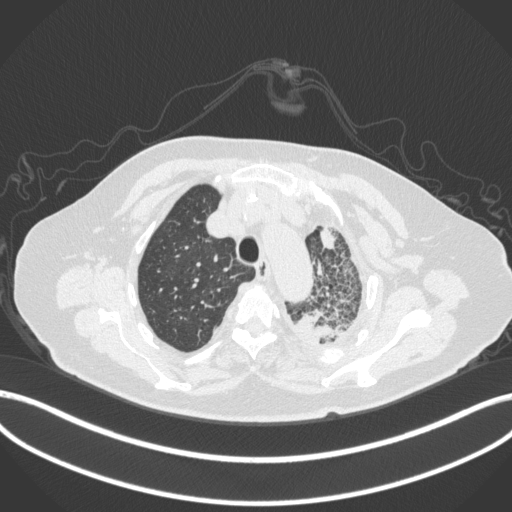
Chest CT, one axial slice. Position 315 of 399 along the scan axis. Reconstruction kernel B31f. 120 kVp. Lung window (W 1500 / L -600 HU). 512 × 512 image matrix, field of view 400 × 400 mm. Patient: female, 75 years. From the clinical record (not read from this slice): clinical TNM (as recorded): T3 N3 M1.
Structures marked on this image (rectangle marked by the reading radiologist):
- lung tumour (recorded histology: adenocarcinoma): bounding box [x1, y1, x2, y2] px = [294, 304, 344, 348]